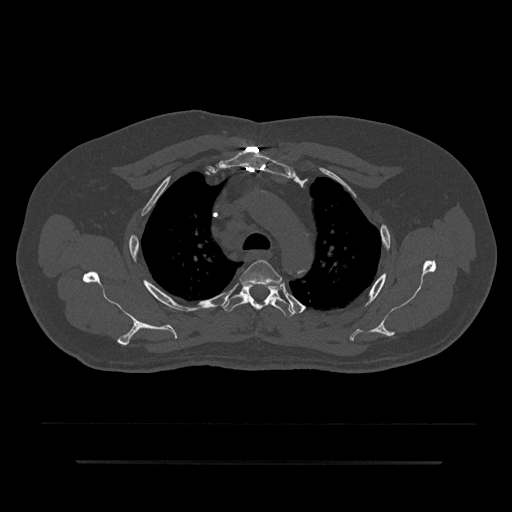
CT including the spine, one axial slice. Position 634 of 797 along the scan axis. Reconstruction kernel Br40s/3. 120 kVp. Bone window (W 1800 / L 400 HU). 512 × 512 image matrix, field of view 464 × 464 mm. Patient: male, 59 years. From the clinical record (not read from this slice): primary cancer: bile ducts; vertebrae with lytic lesions (as recorded): T10.
Structures marked on this image (semi-automatically segmented with operator editing):
- T3 vertebra: bounding box [x1, y1, x2, y2] px = [240, 260, 282, 286]
- T4 vertebra: [222, 283, 294, 317]